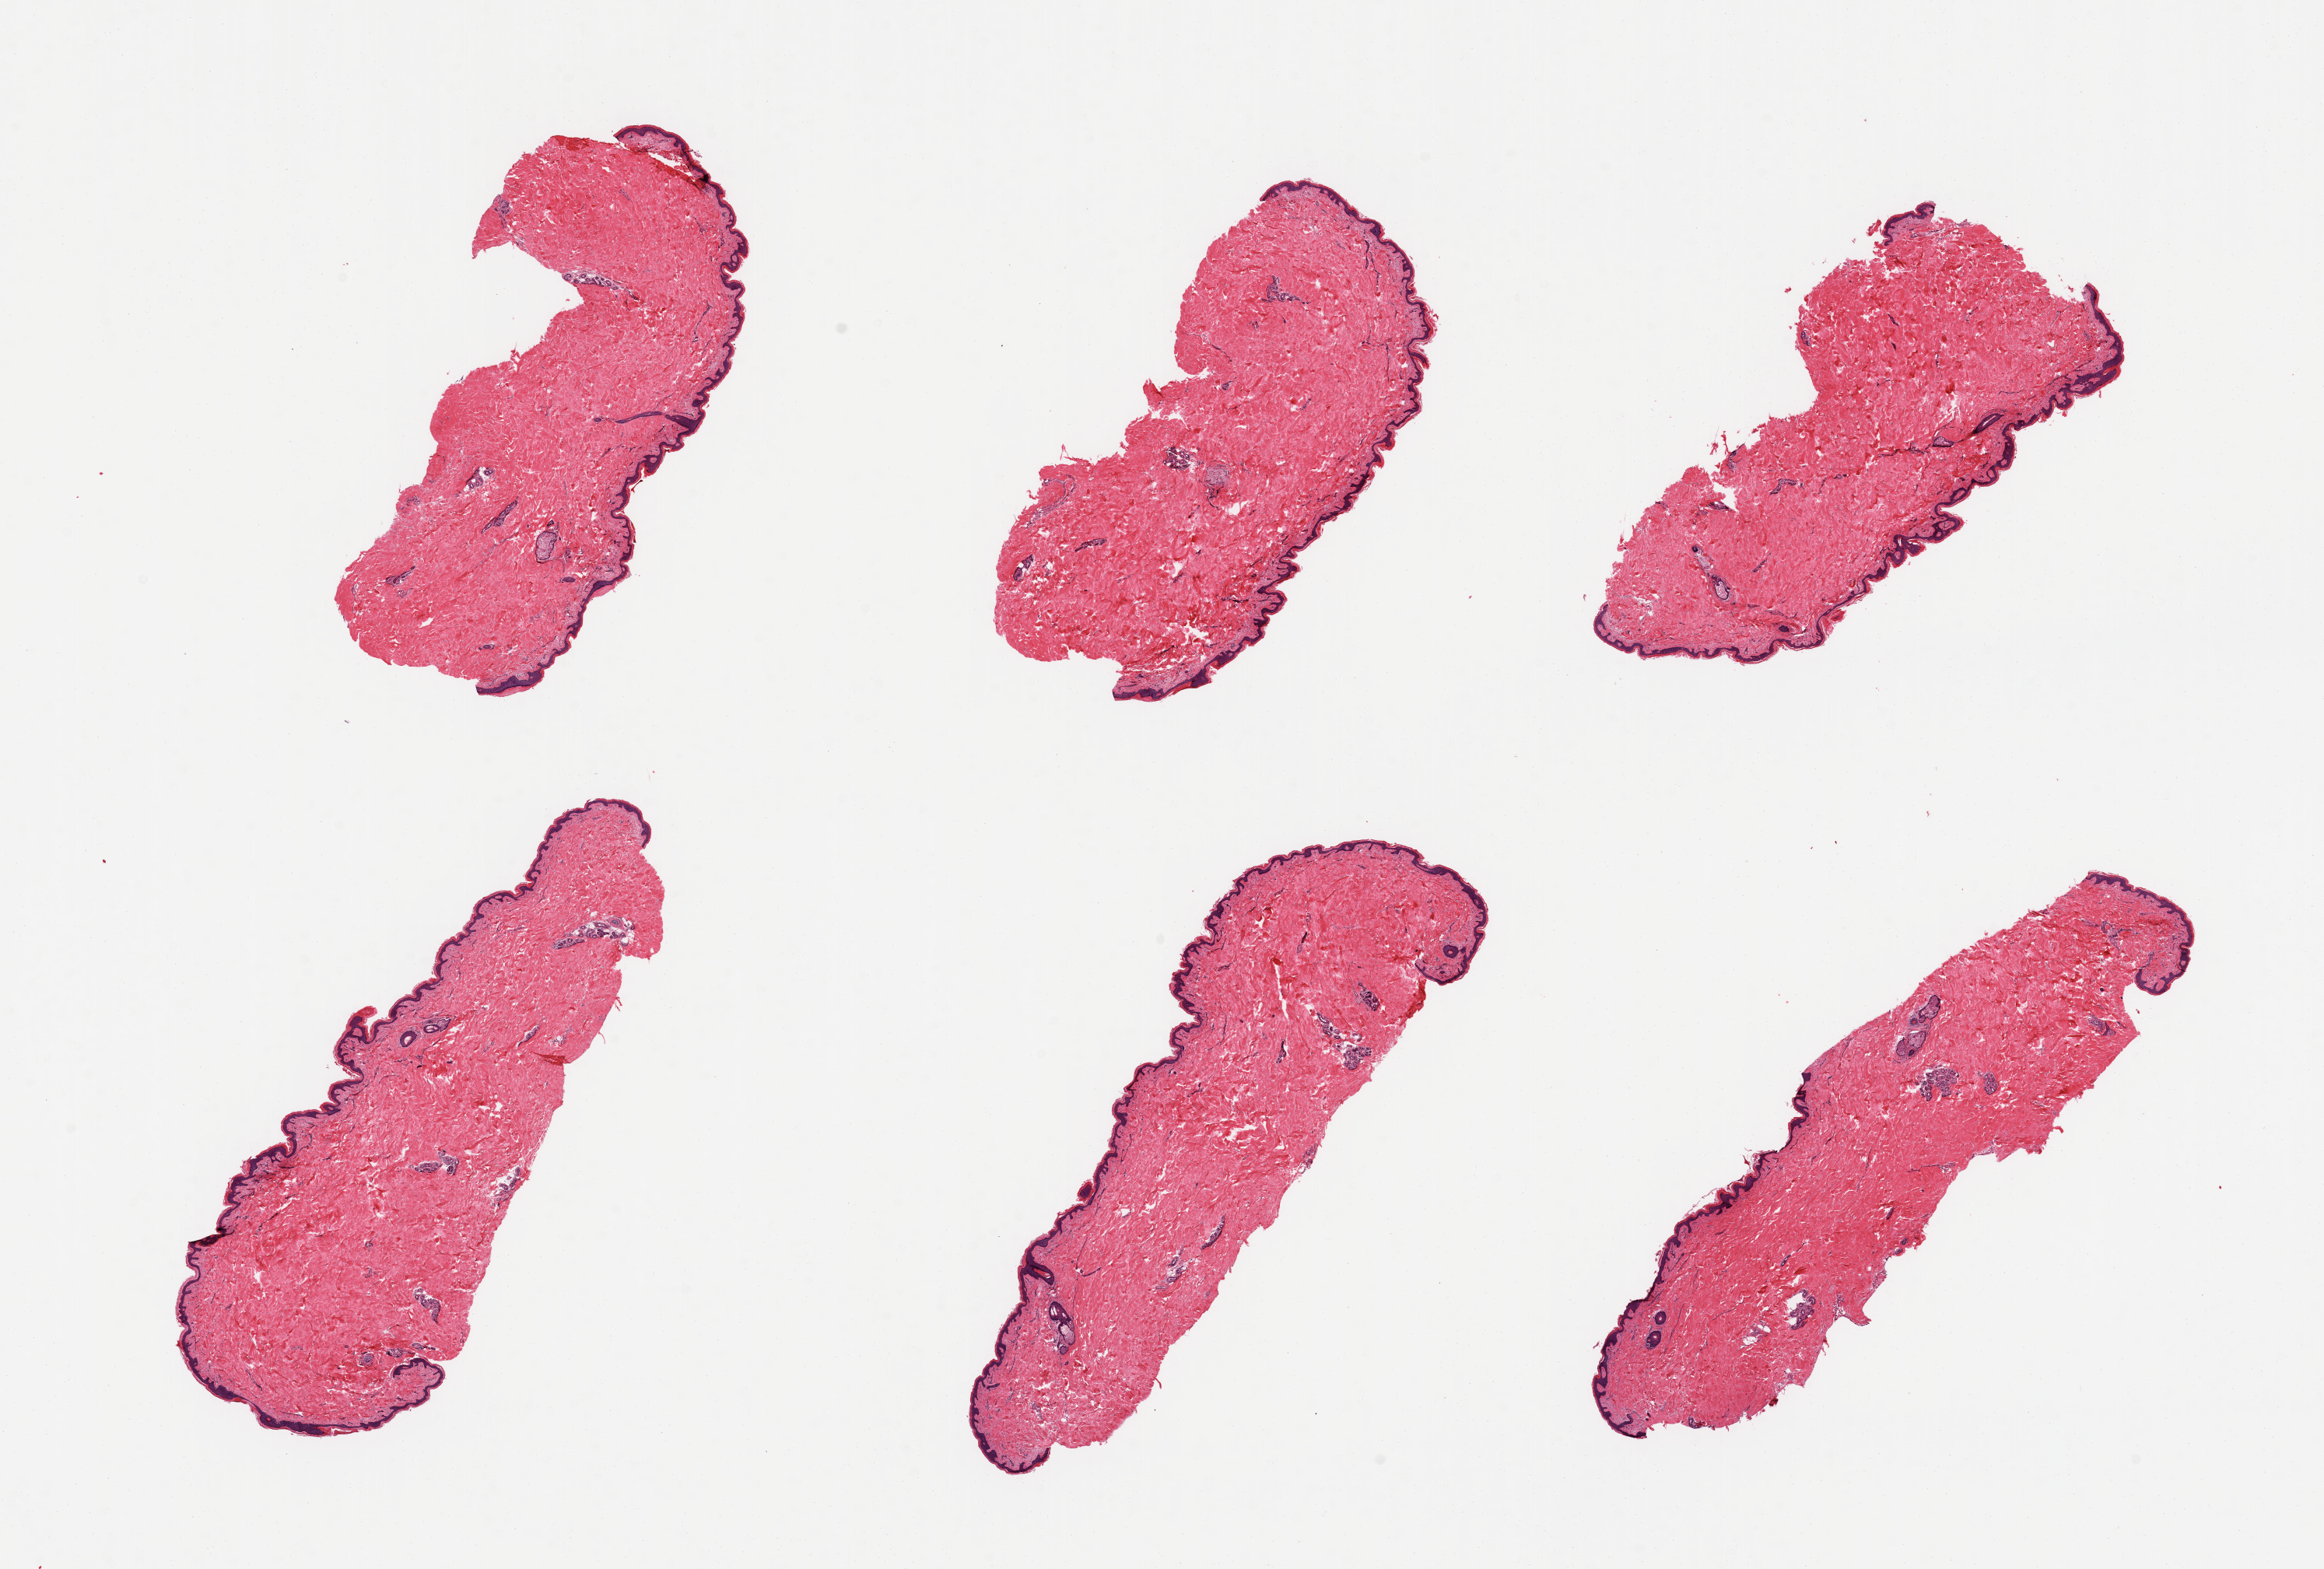
Digitized haematoxylin and eosin-stained section — shown as a low-resolution overview of the whole scanned area (about 23.6 x 16.0 mm, slide scanned at 20x), PAXgene-fixed, paraffin-embedded tissue, section of skin of suprapubic region (target tissue), donor tissue sample. Donor sex: male.
- reviewer comment on this tissue sample: 6 pieces, squamous epithelium is ~50 microns